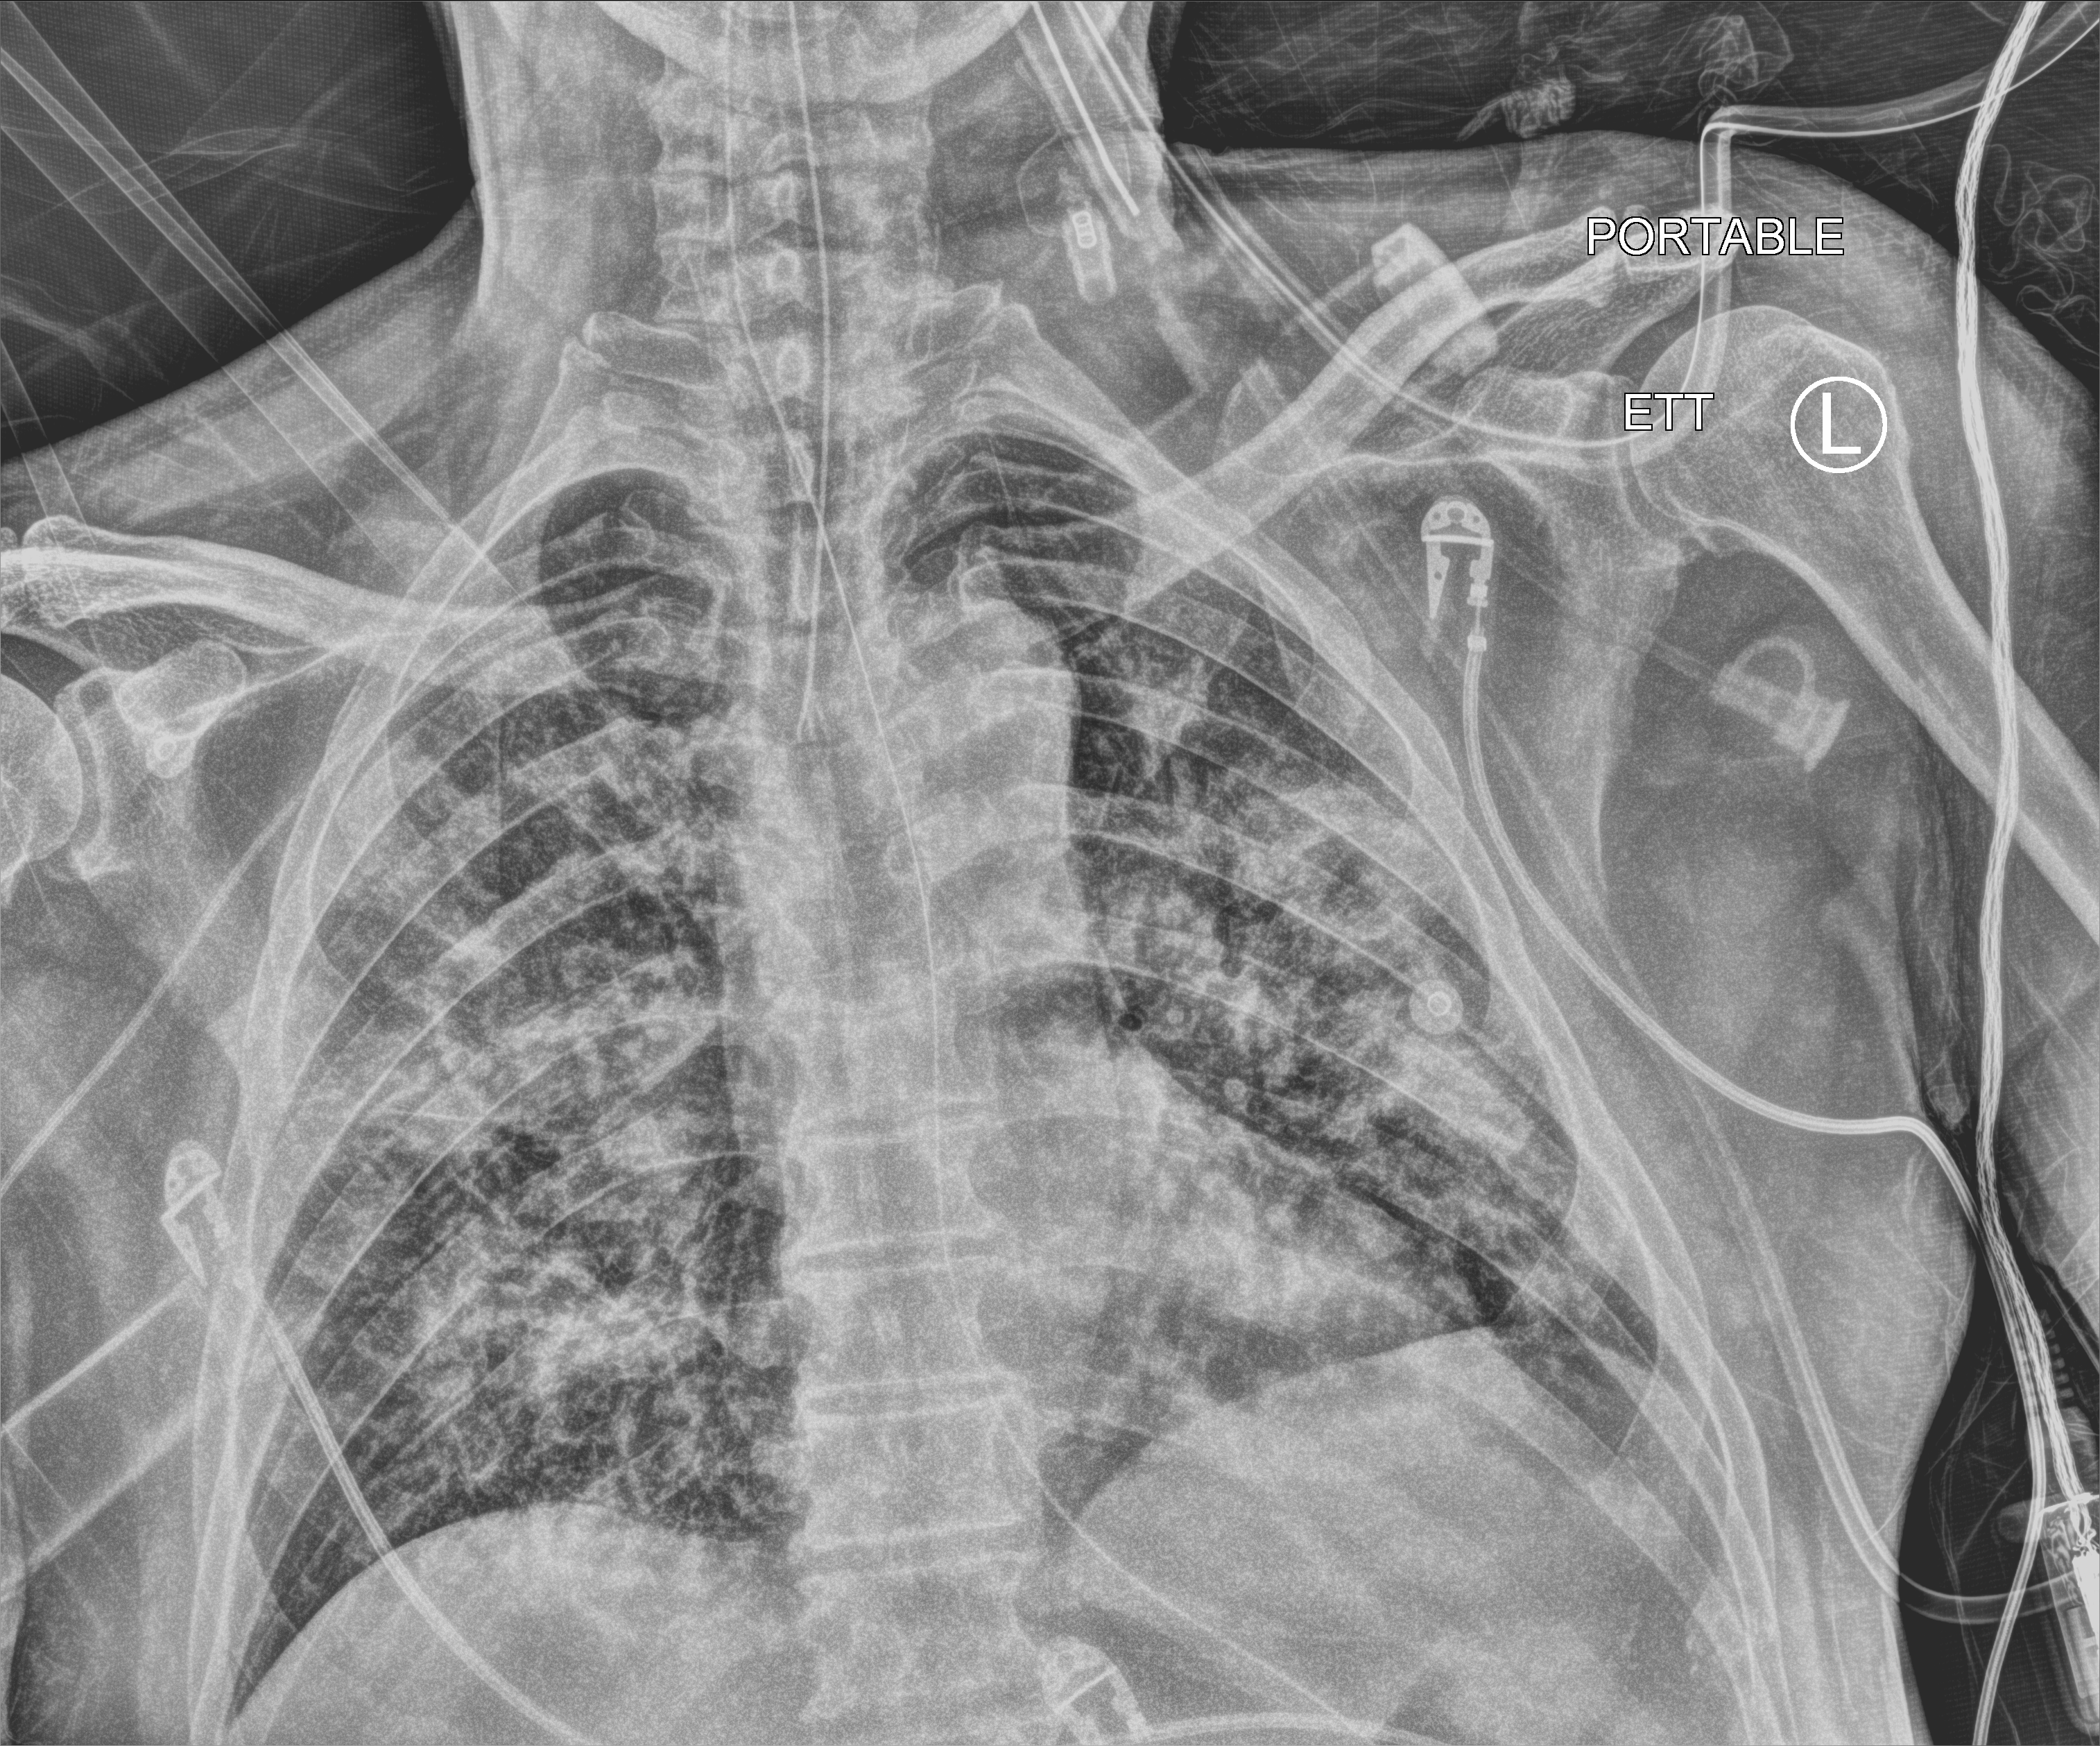
Bedside chest radiograph (computed radiography), anteroposterior (AP) projection. Patient hospitalised with COVID-19; male, aged 60–74 years.
Hospital-stay facts (about this admission, not read from this image; timing relative to this image not recorded): mechanically ventilated during this hospital stay: yes; length of hospital stay: 20 days.